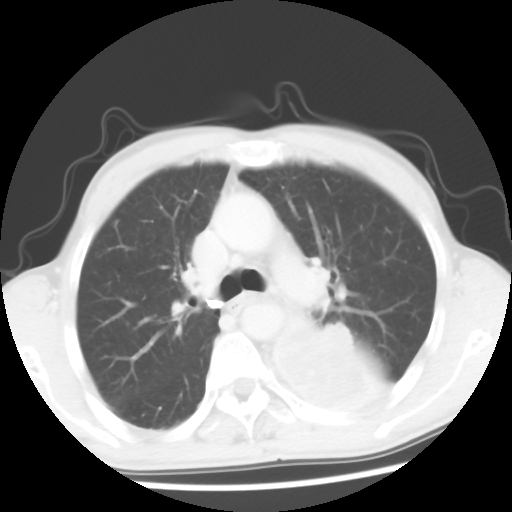
Chest CT, one axial slice; position 38 of 56 along the scan axis; reconstruction kernel STANDARD; 120 kVp; lung window (W 1500 / L -600 HU); 5 mm slice thickness; 512 × 512 image matrix, field of view 318 × 318 mm. Male patient, age 60 years. From the clinical record (not read from this slice): clinical TNM (as recorded): T4 N0 M0.
Structures marked on this image (bounding box drawn by a radiologist):
- lung tumour (recorded histology: squamous cell carcinoma): bounding box [x1, y1, x2, y2] px = [263, 312, 389, 419]